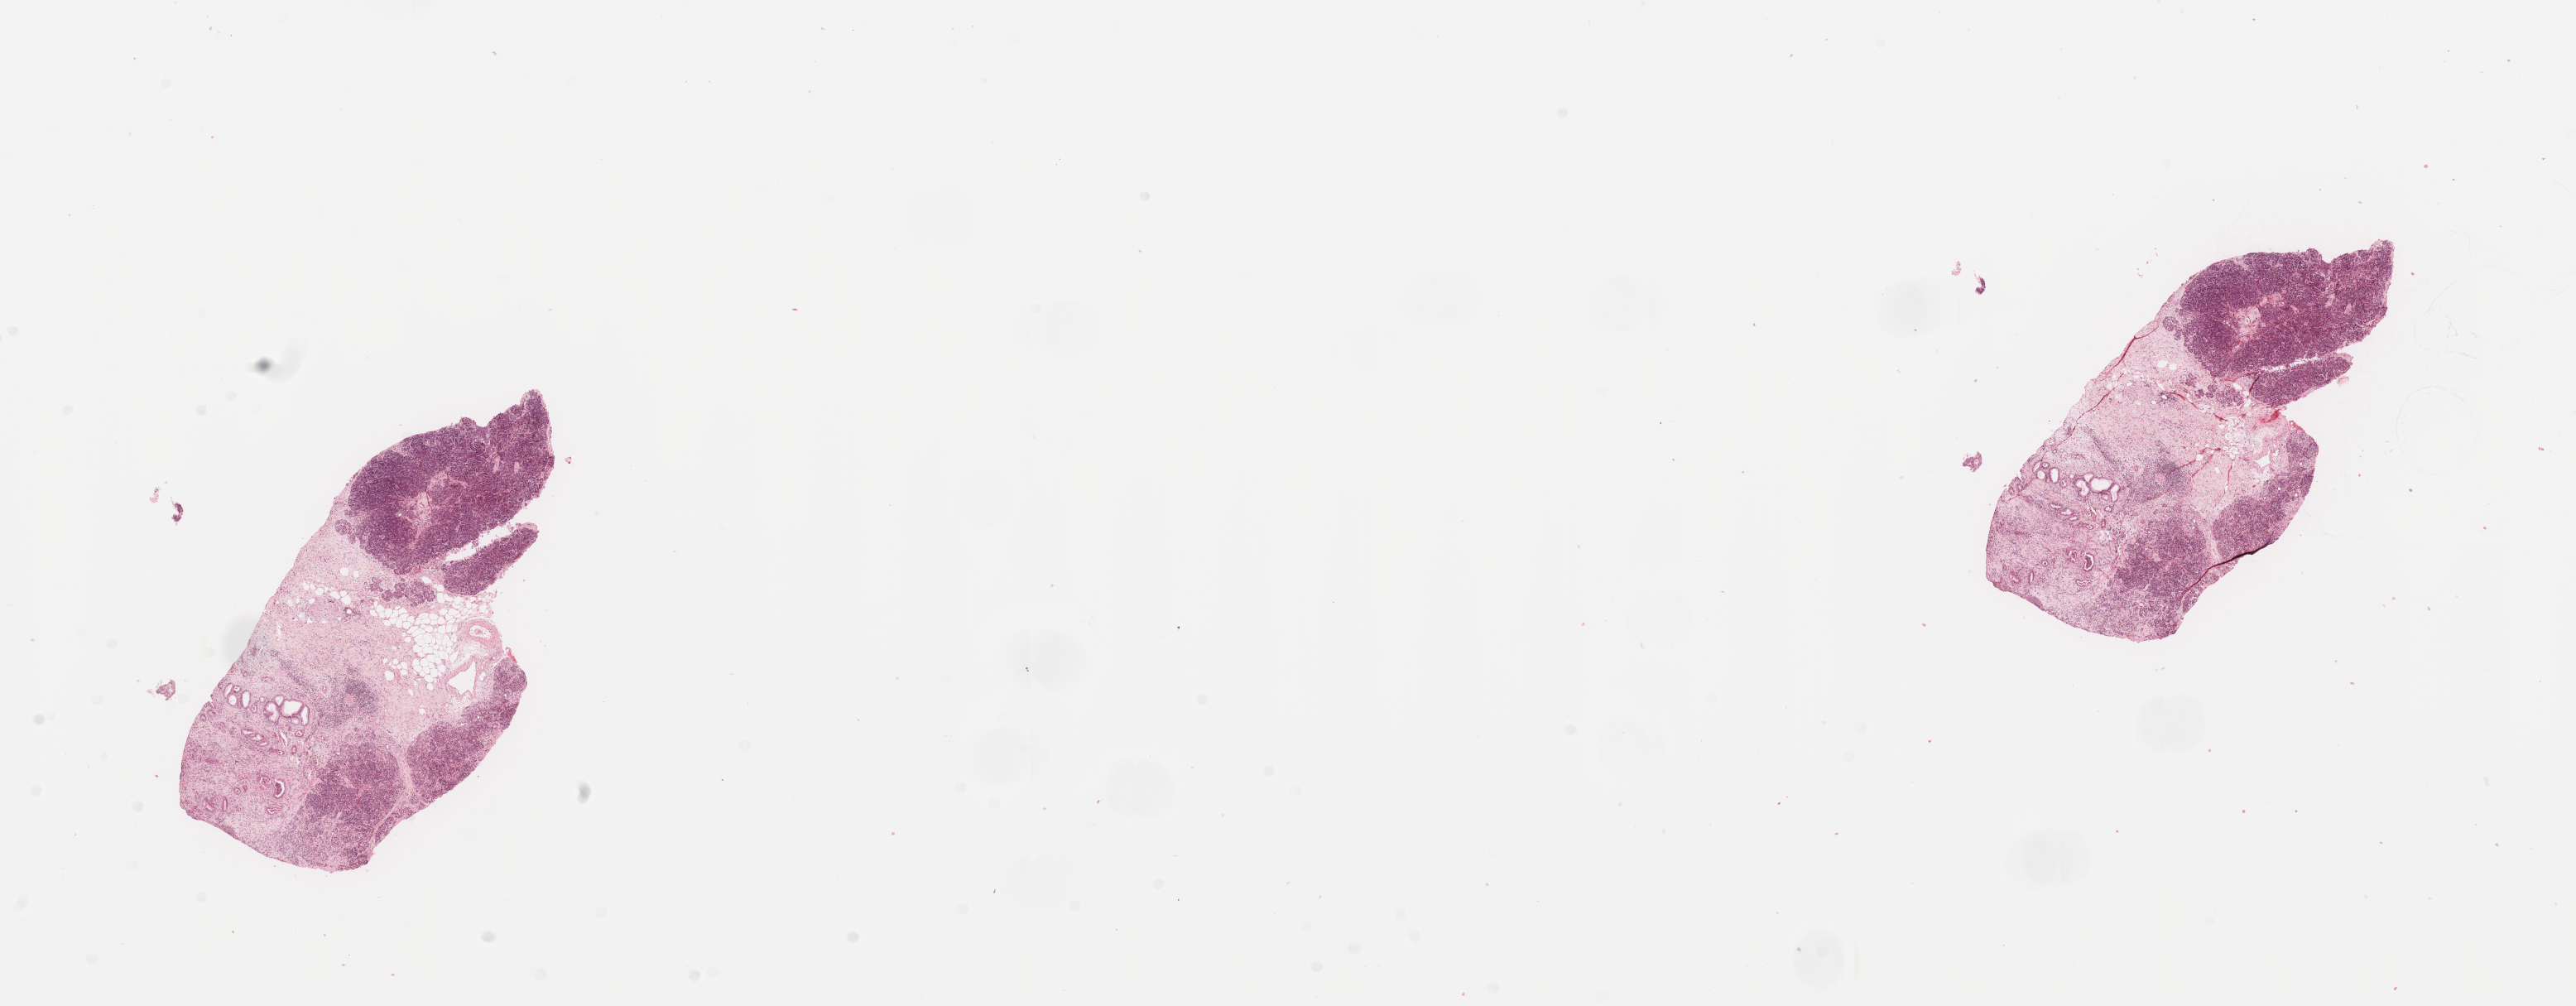
Whole-slide histology image, H&E-stained — low-resolution overview of the scanned area, about 24.6 x 9.6 mm, tumour tissue sample, sampled site: pancreas. Male, 71 y/o. Histologic grade: G2 (moderately differentiated). Slide review estimates, as recorded: tumour nuclei 10%, necrosis 0%.
AJCC pathologic stage: IB. Primary tumour site (as recorded): head. Histologic diagnosis: Infiltrating duct carcinoma, NOS.